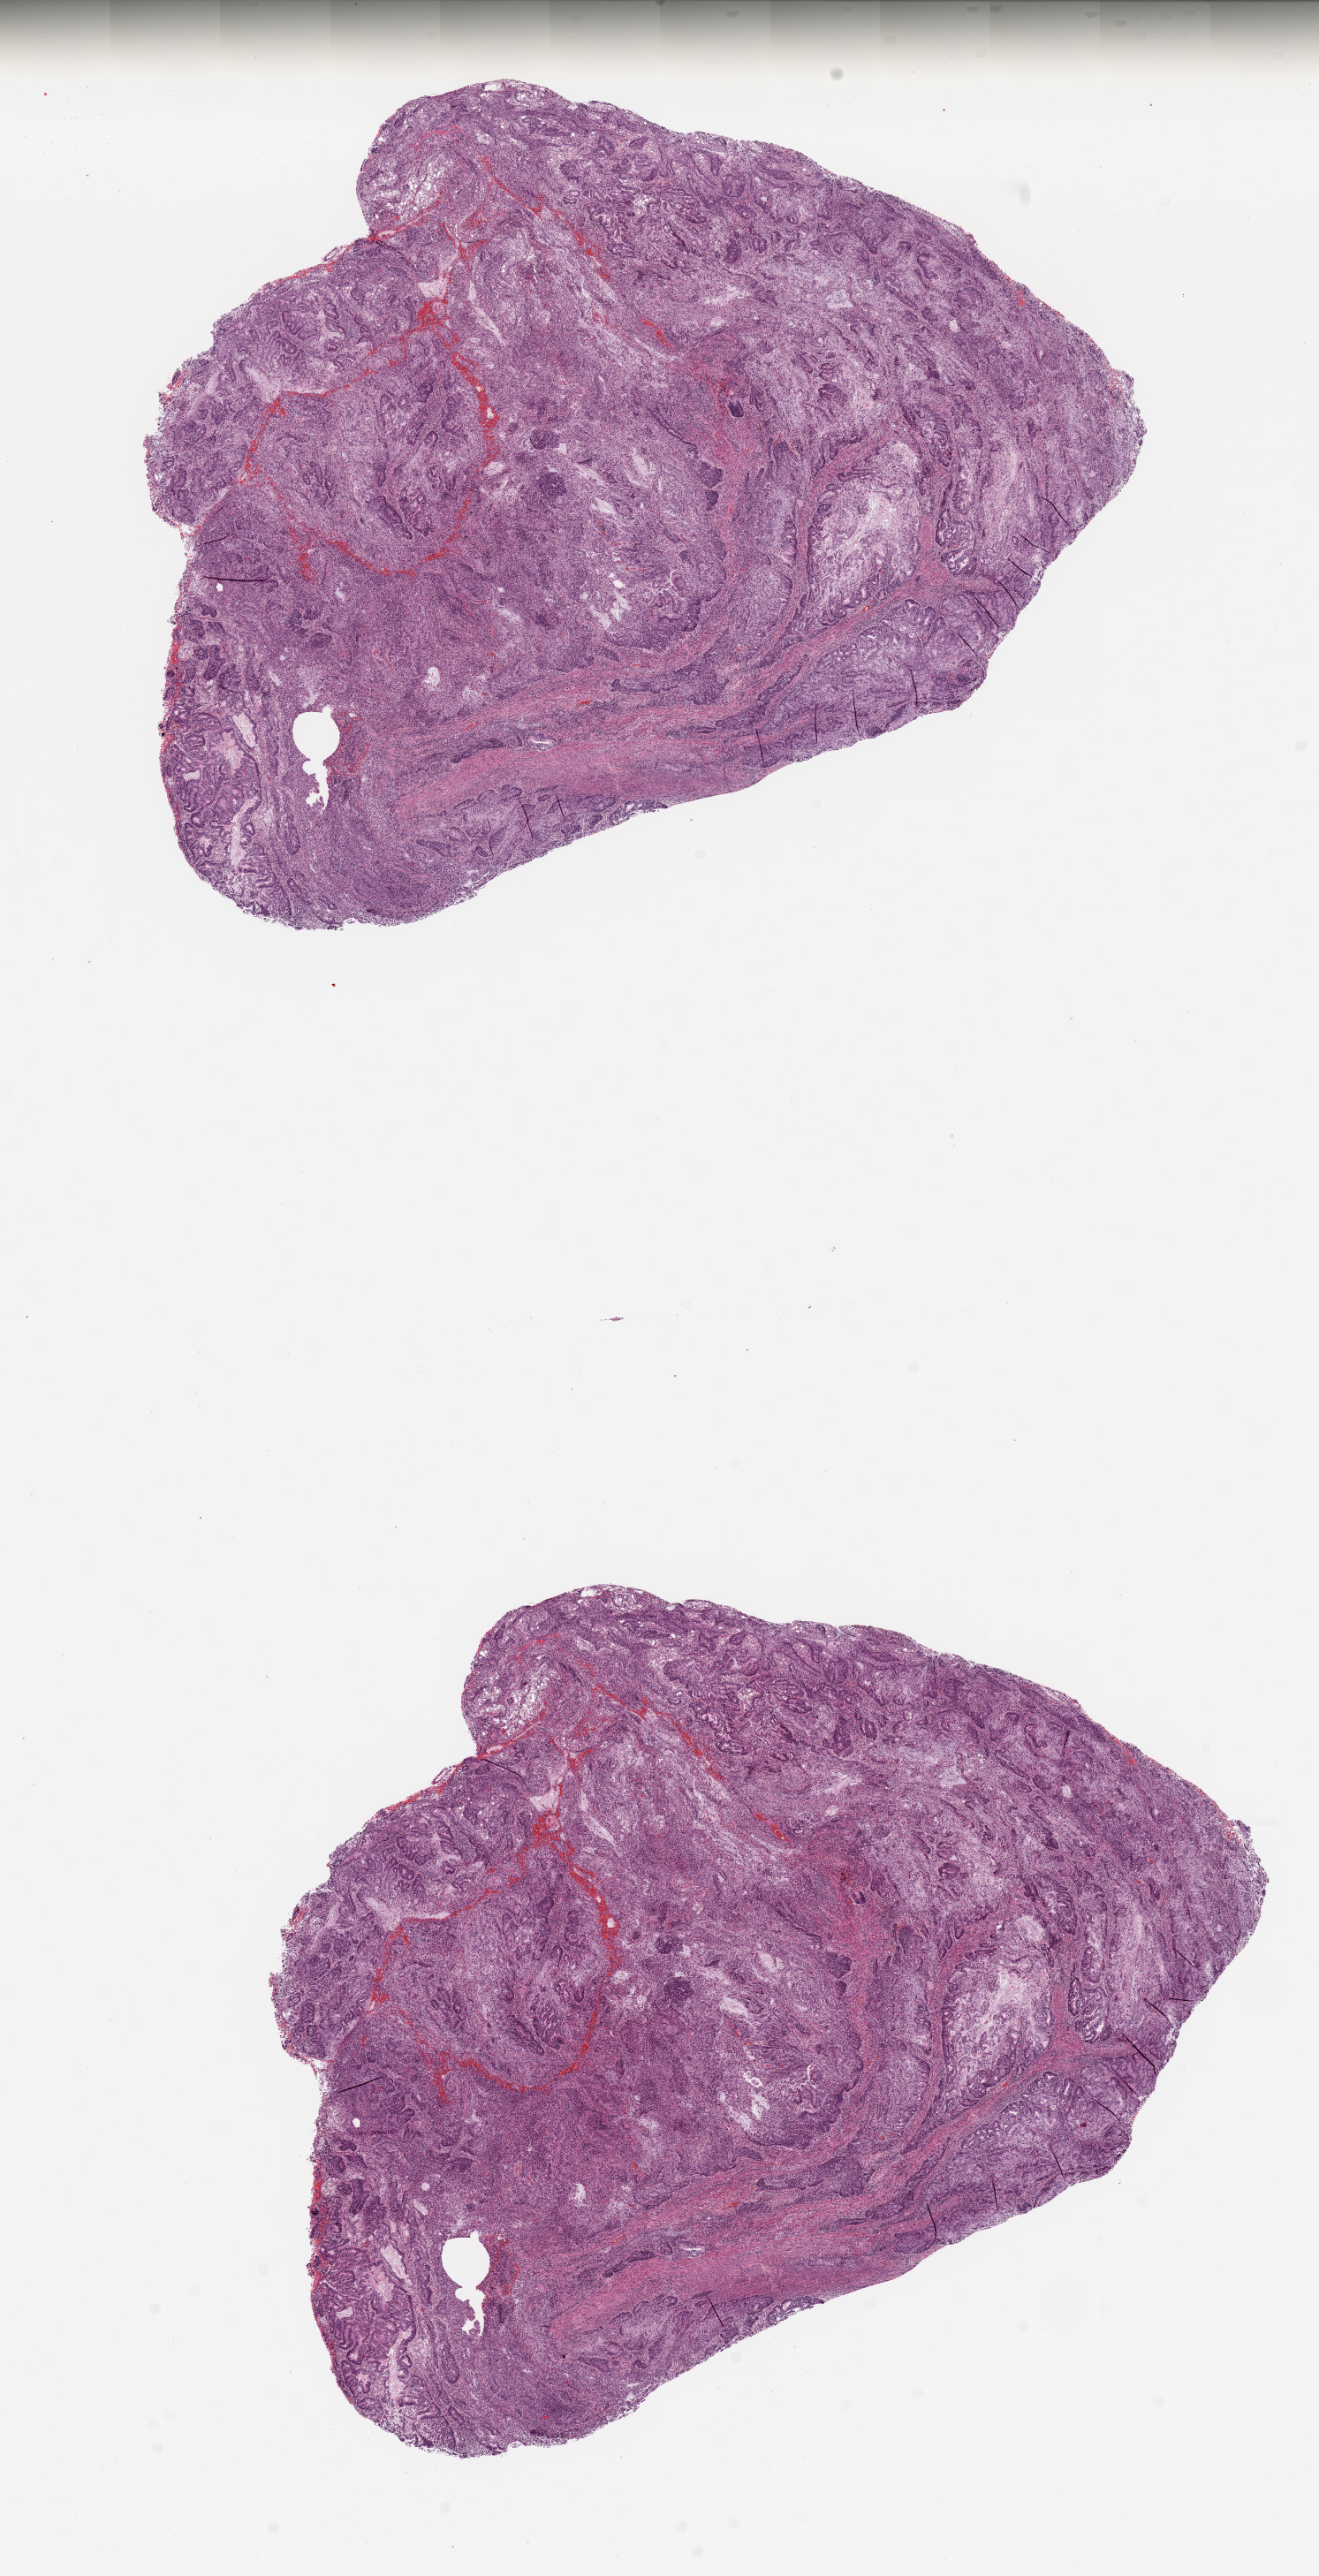
Whole-slide histology image, H&E-stained — a low-resolution overview of the entire scanned area, about 11.8 x 23.1 mm (from a 20x scan). Tumour tissue sample, sampled site: uterus. Patient: female, age 56 years. Histologic grade: G1 (well differentiated). Composition of this section per pathologist review: tumour nuclei 80%, necrosis 5%.
Diagnosis: Endometrioid adenocarcinoma, NOS. Primary tumour site (as recorded): anterior endometrium. AJCC pathologic stage: I.